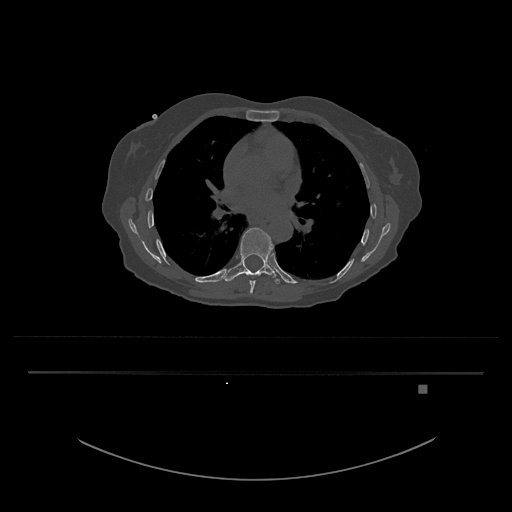
CT including the spine, one axial slice. Slice 773 of 797 in the series (ordered by position). Bone window (W 1800 / L 400 HU). 512 × 512 image matrix. Patient: female, 57 years. From the clinical record (not read from this slice): primary cancer: cervical.
Annotated regions visible in this slice (semi-automatically segmented with operator editing):
- T8 vertebra: box from (x=244, y=273) to (x=259, y=294) px
- T9 vertebra: (x=223, y=227)–(x=281, y=284)